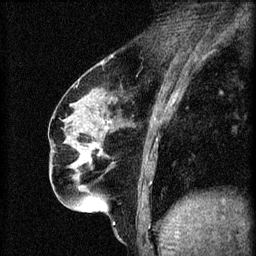
Breast MRI (dynamic contrast-enhanced), one sagittal slice; position 24 of 60 along the scan axis; 3 images stored at this slice position (order not interpretable as contrast timing); 1.5 T; TE 4.2 ms, TR 8.2 ms; 2 mm slice thickness; 256 × 256 image matrix, field of view 180 × 180 mm. Female patient, age 56 years.
Outlined on this slice (semi-automatic segmentation, software-assisted and operator-edited):
- analysis volume of interest (the breast-tissue region the enhancement analysis was run in; not a lesion): bounding box [x1, y1, x2, y2] px = [67, 136, 111, 179]
- tumour enhancement mask (voxels above the 70 % enhancement threshold inside the analysis volume of interest): [79, 152, 88, 161]